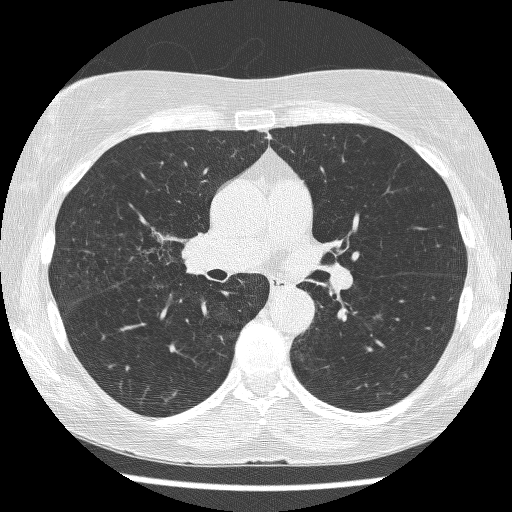
Axial slice from a low-dose chest CT screening exam. First (baseline) screen. Lung window (W 1500 / L -600 HU). 1.25 mm slice thickness. Lung (sharp) reconstruction kernel (BONE). Slice 159 of 271 in the series. 512 × 512 image matrix. Female, age 64 years at enrolment.
Expert-annotated lung lesion, bounding box <121,211,196,268> (left, top, right, bottom; pixels). The screening reader recorded 3 non-calcified nodules or masses ≥4 mm on this exam; which of them this box marks is not recorded. Official screen result: positive, change unspecified: nodule(s) >= 4 mm or enlarging nodule(s), mass(es), or other non-specific abnormalities suspicious for lung cancer. Lung cancer was diagnosed 735 days after this screen: adenocarcinoma, NOS, right upper lobe, right middle lobe, right hilum, stage IV (AJCC 6th edition), 85 mm at pathology.